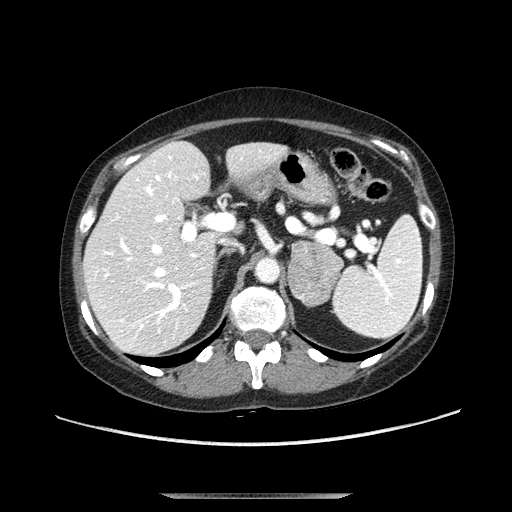
Contrast-enhanced abdominal CT, one axial slice; position 69 of 107 along the scan axis; soft-tissue window (W 400 / L 40 HU); 512 × 512 image matrix, field of view 380 × 380 mm. Female patient. From the clinical record (not read from this slice): diagnosis: adrenocortical carcinoma; tumour side: left adrenal; tumour size at pathology: 7.5 cm; Ki-67 index: 9 %; stage (as recorded): 3.
Annotated regions visible in this slice (semi-automatically segmented with operator editing):
- mass: bounding box [x1, y1, x2, y2] px = [288, 241, 344, 305]